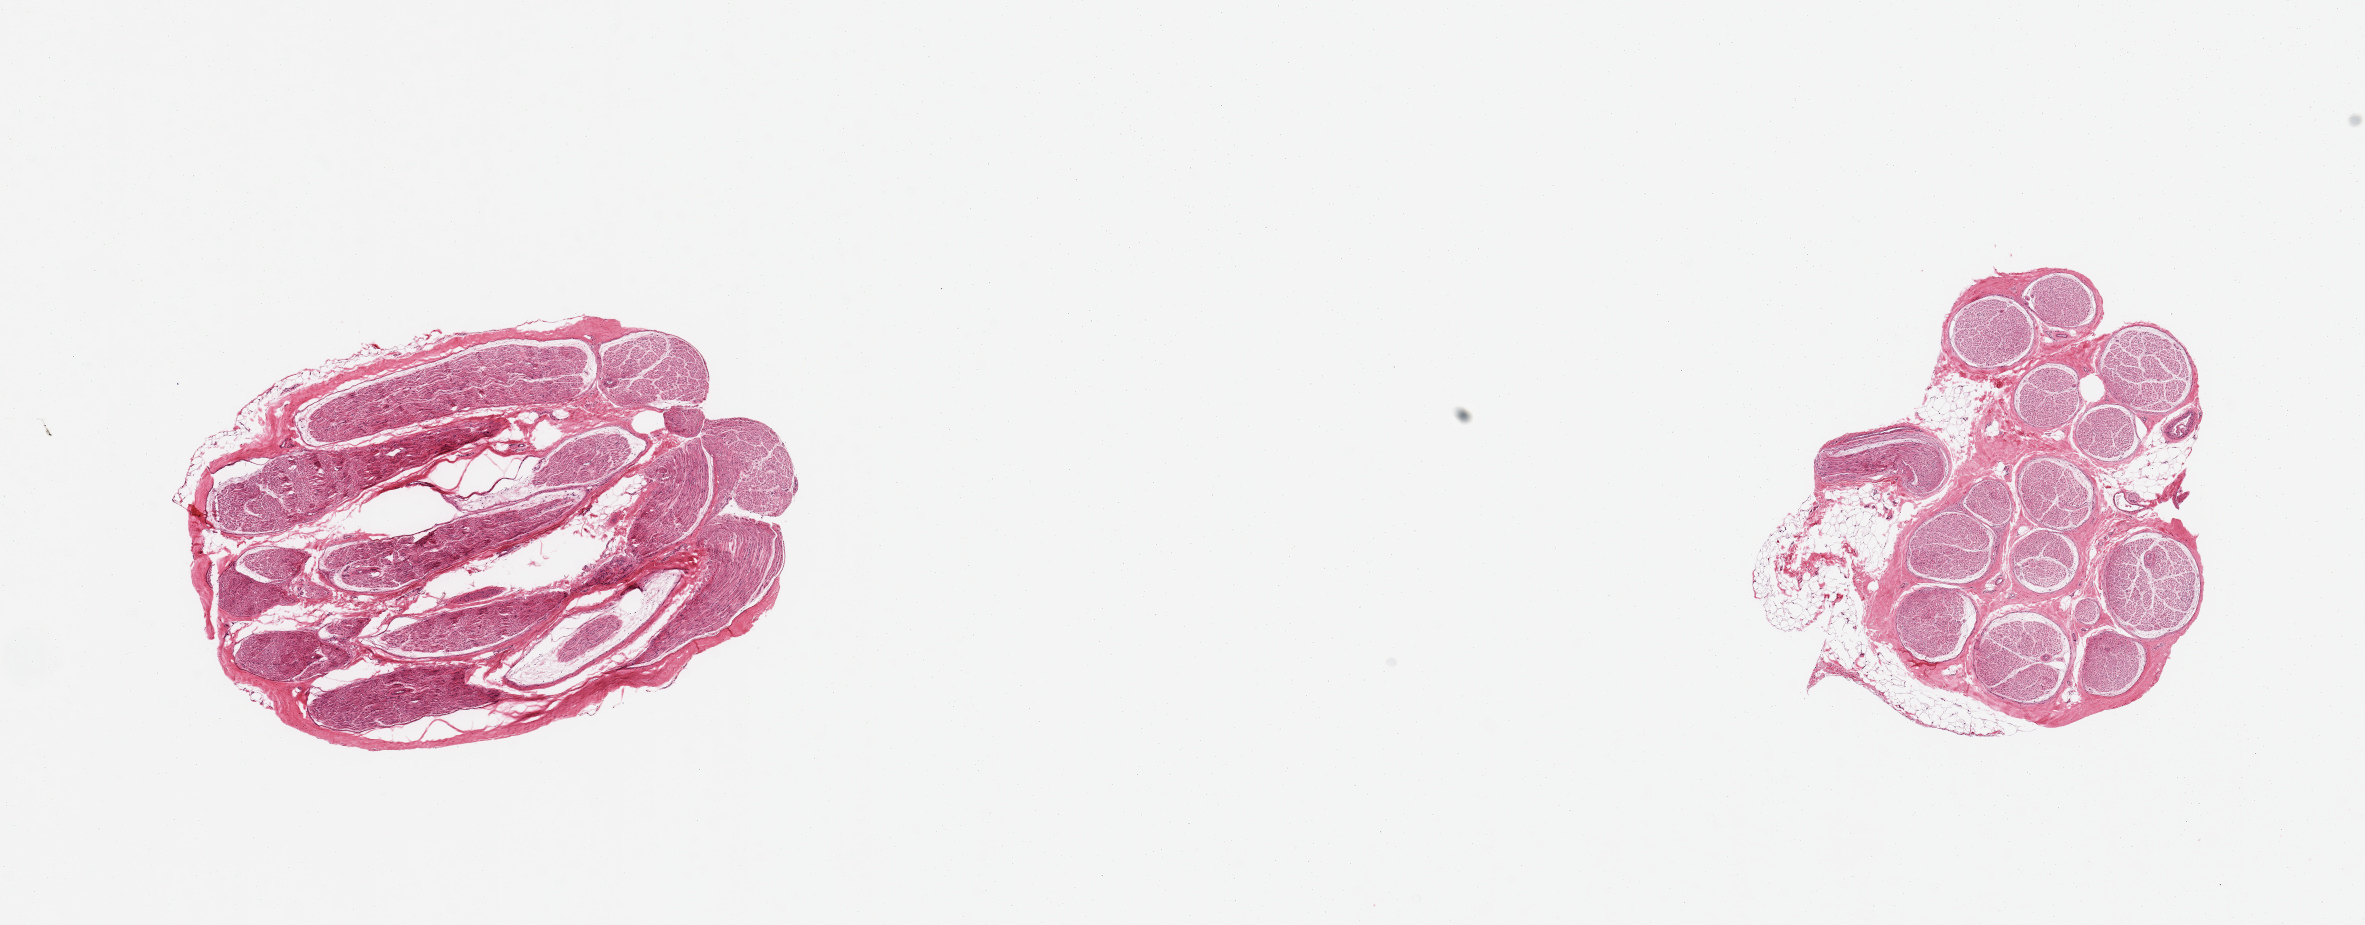
Haematoxylin and eosin whole-slide image, shown as a low-resolution overview of the whole scanned area (about 18.7 x 7.3 mm). PAXgene-fixed paraffin-embedded (PFPE) section. Target tissue: tibial nerve. Tissue donor sample. Donor sex: male.
Pathologist's review note for this sample: 2 pieces, minimal adherant fat.